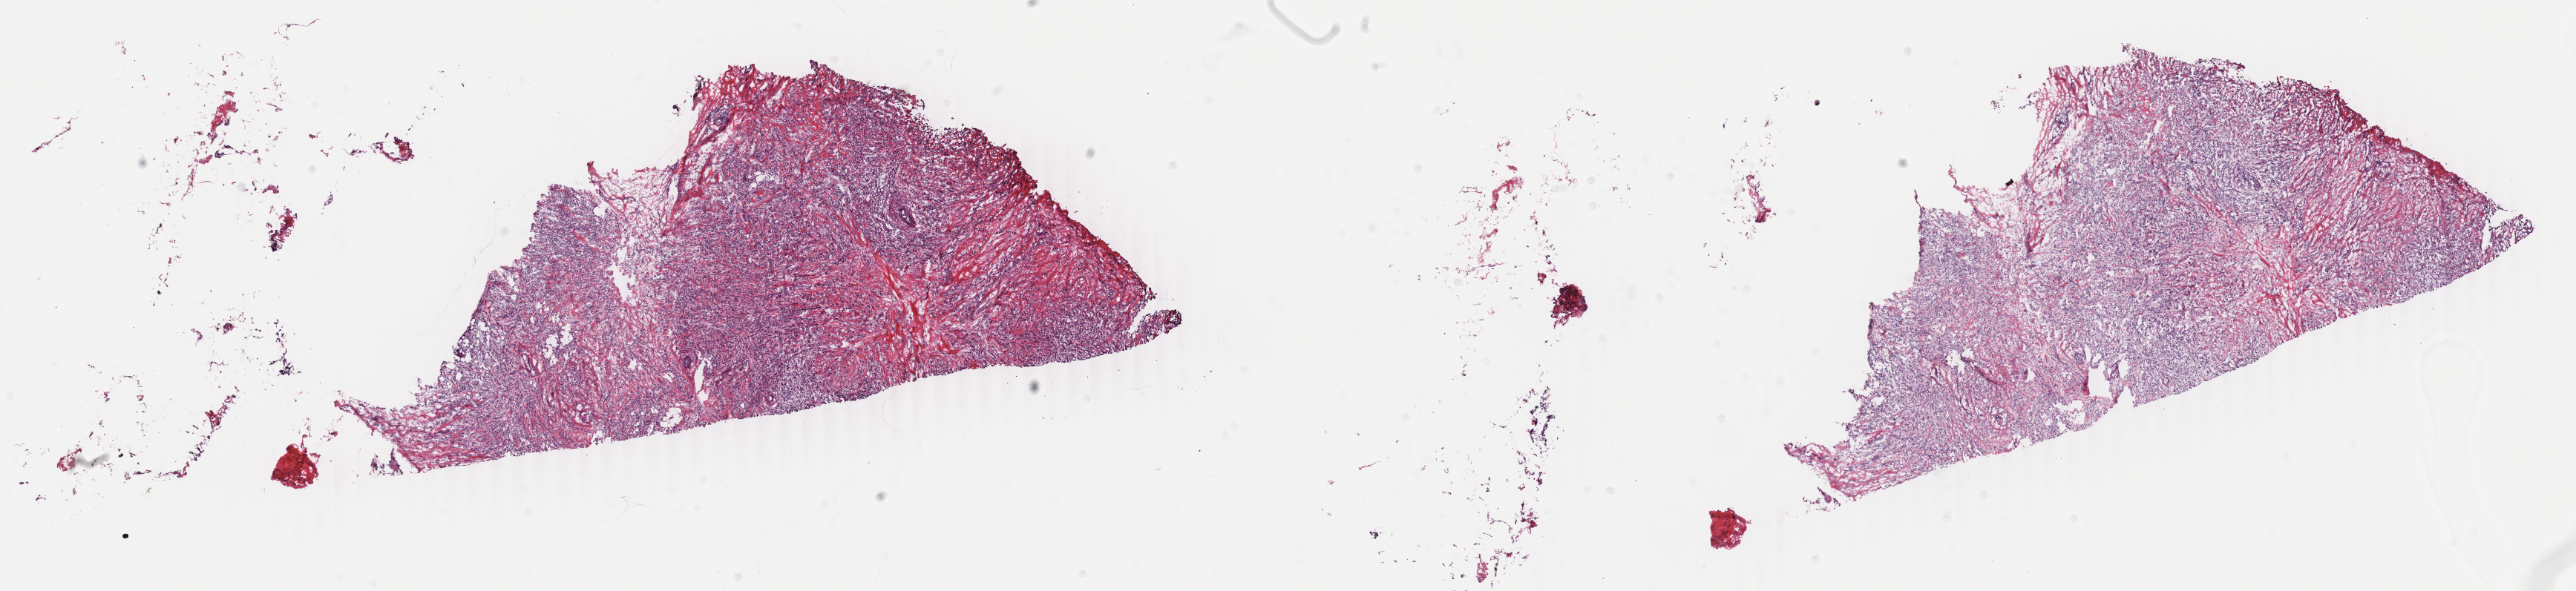
Digitized Hematoxylin and eosin (H&E) stained tissue section (whole slide) — shown as a low-resolution overview of the whole scanned area (about 27.6 x 6.3 mm, from a 40x scan), frozen section, sample: primary tumour, breast. Female patient; age at initial diagnosis 63 years. Pathologist review of this section (percent, as recorded): tumour cells 95%, tumour nuclei 95%, normal cells 0%, stromal cells 4%, necrosis 1%. Infiltration values recorded for this section: lymphocyte infiltration 1%, monocyte infiltration 0%, neutrophil infiltration 0%.
• diagnosis: Lobular carcinoma, NOS
• TNM: T3 N0 (i+) M0
• AJCC pathologic stage: IIB
• laterality: left
• lymph nodes positive (case pathology): 0 of 2 examined